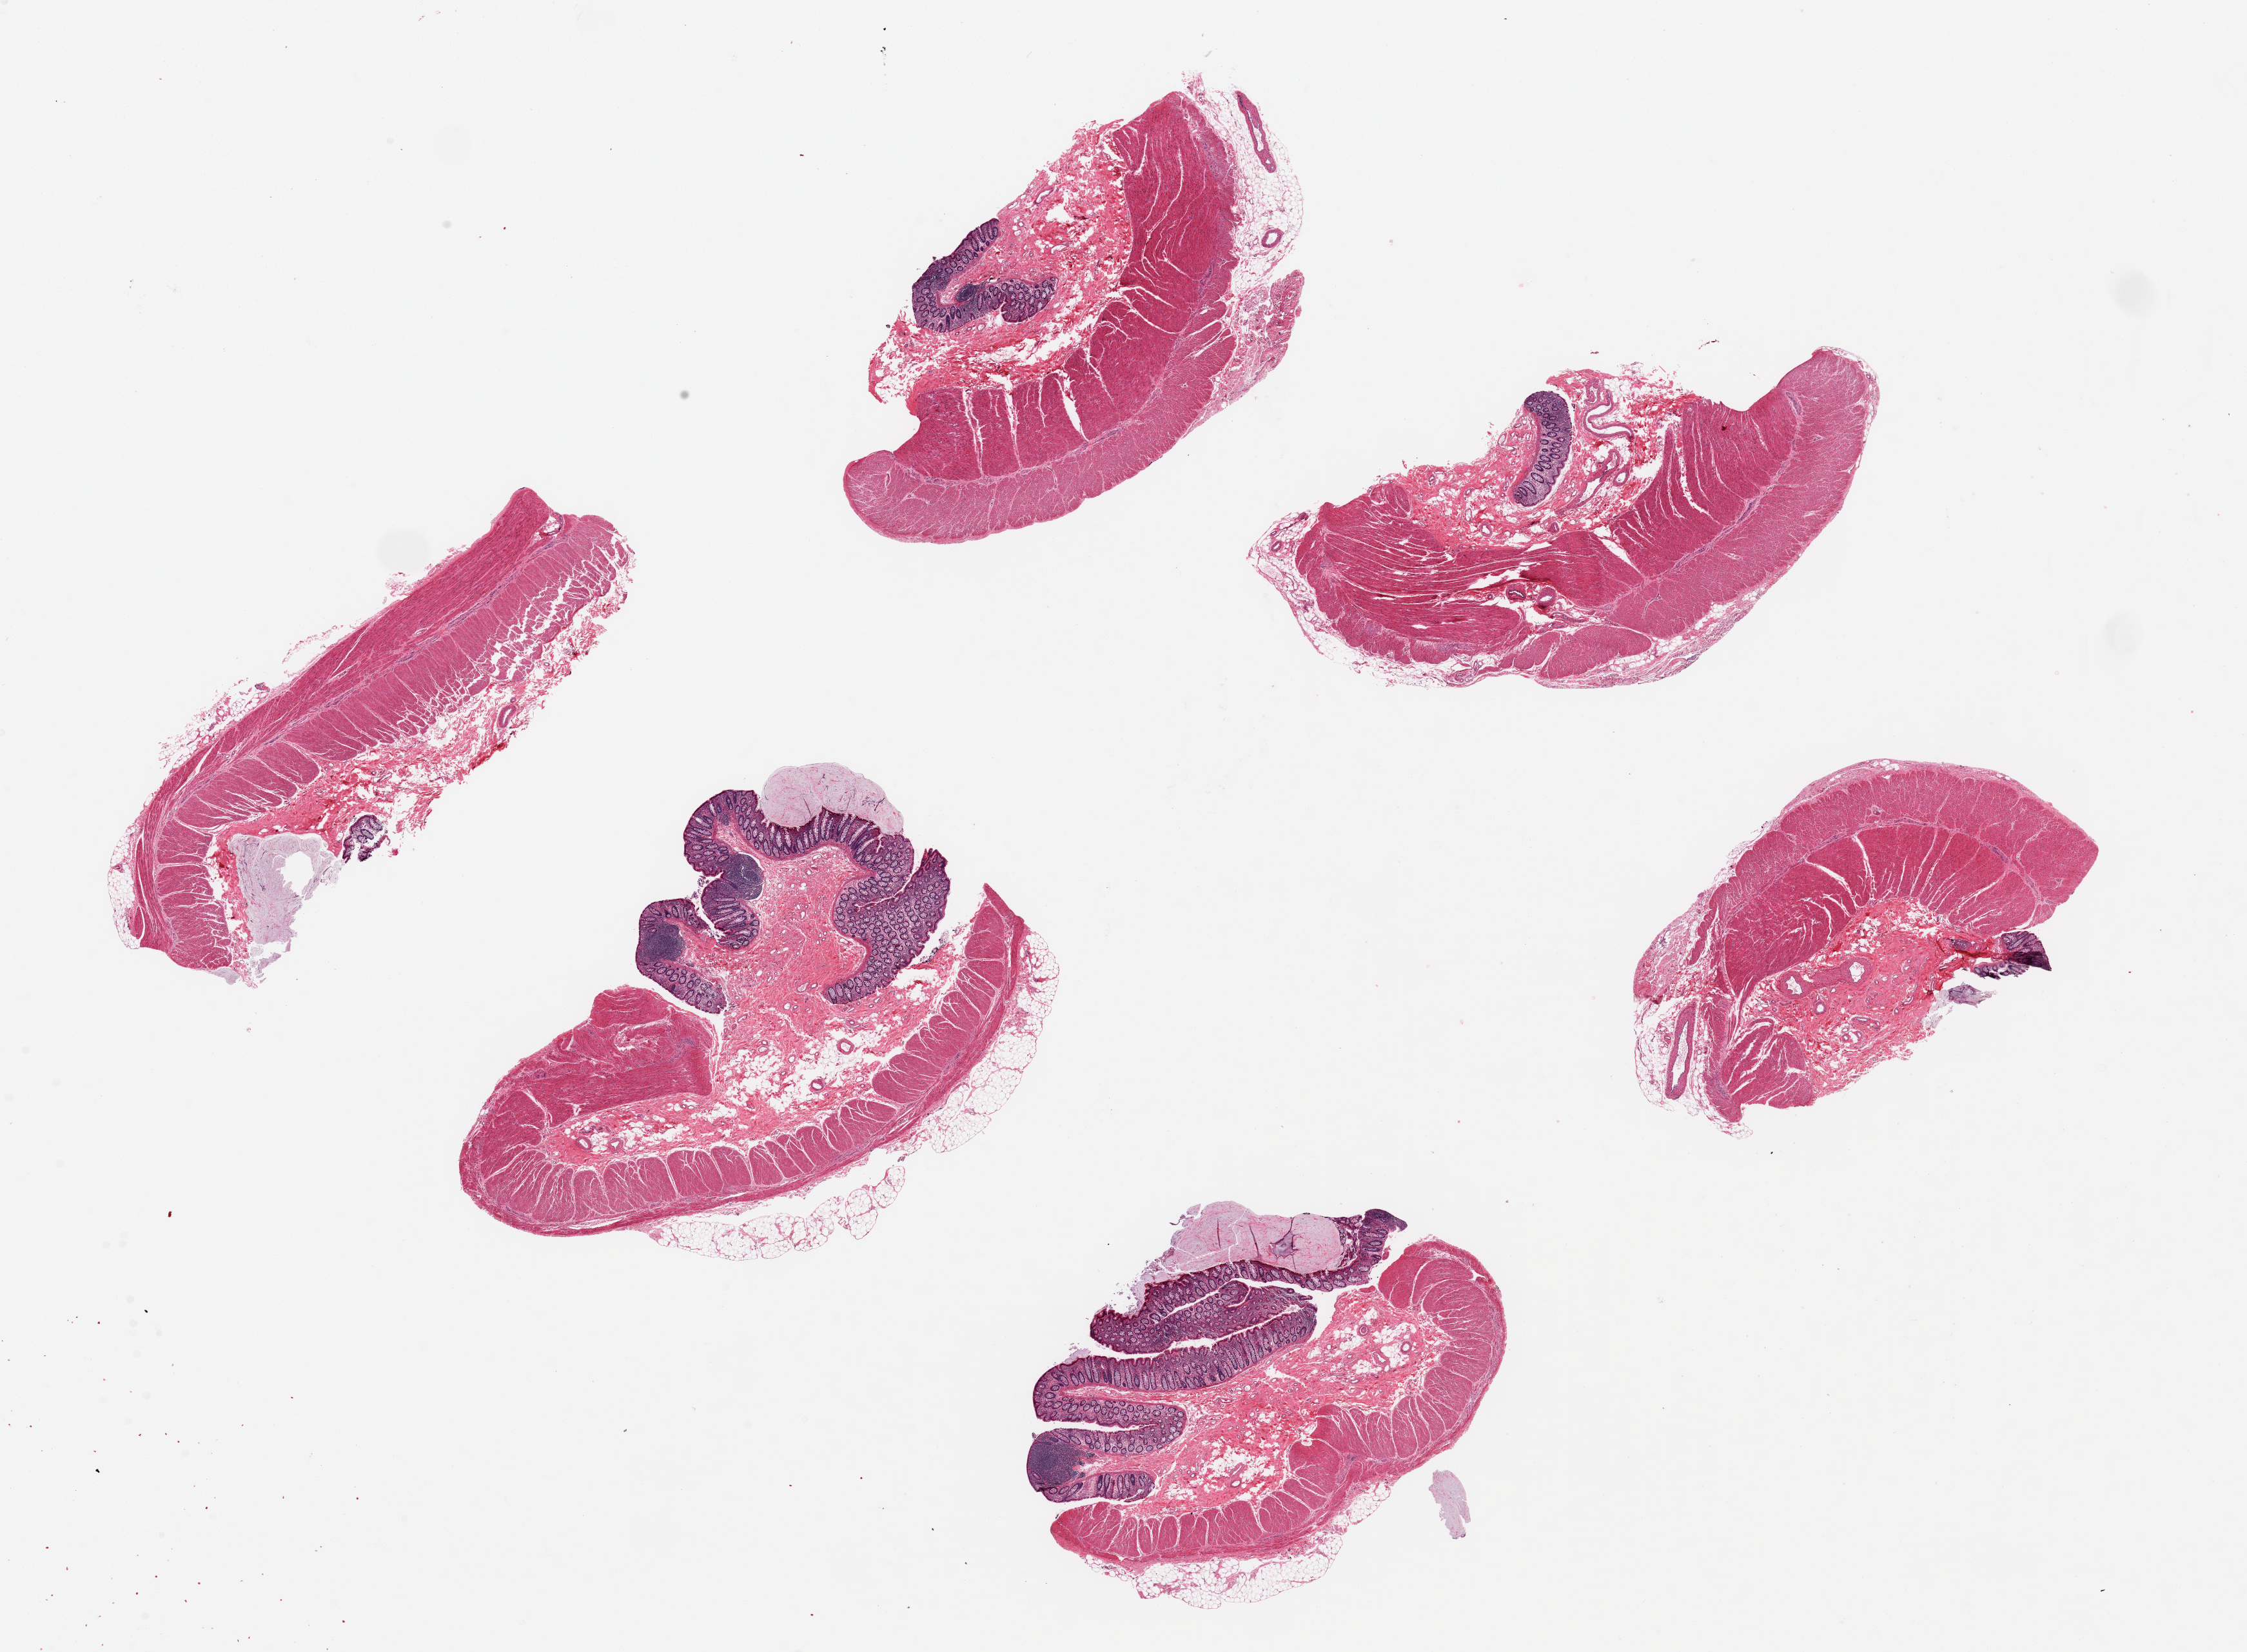
Hematoxylin and eosin (H&E) whole-slide image, brightfield, low-resolution overview of the scanned area, about 27.6 x 20.3 mm; PAXgene-fixed paraffin-embedded (PFPE) section; section of transverse colon (target tissue); donor tissue sample. Donor: female.
Review note (as recorded): 6 pieces, ~6x4 mm; only 2 have abundant mucosa.